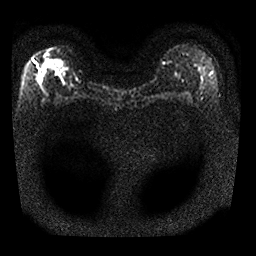
Breast MRI, one axial slice; position 15 of 25 along the scan axis; diffusion-weighted series; image 2 of 4 stored at this slice position (different b-values; order by instance number); 1.5 T; 4 mm slice thickness; 256 × 256 image matrix, field of view 300 × 300 mm. Female patient.
Annotated regions visible in this slice (outlined manually by an expert reader):
- tumour on diffusion-weighted imaging: bounding box (x1, y1, x2, y2) in pixels: (40, 68, 46, 82)